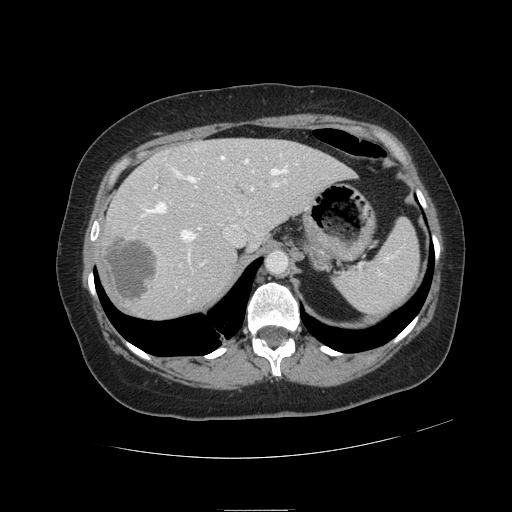
Contrast-enhanced abdominal CT, one axial slice; intravenous contrast given; soft-tissue window (W 400 / L 40 HU); 2.5 mm slice thickness; 512 × 512 image matrix, field of view 400 × 400 mm. Female patient, age 52 years. From the clinical record (not read from this slice): diagnosis: colorectal cancer liver metastases, imaged before liver resection.
Outlined on this slice (outlined manually by an expert reader):
- hepatic veins: bounding box <141,149,288,288> (left, top, right, bottom; pixels)
- liver: <102,139,350,317>
- planned liver remnant (the part of the liver to remain after resection): <168,139,351,245>
- portal vein (with intrahepatic branches): <153,158,286,291>
- liver metastasis: <106,236,157,303>